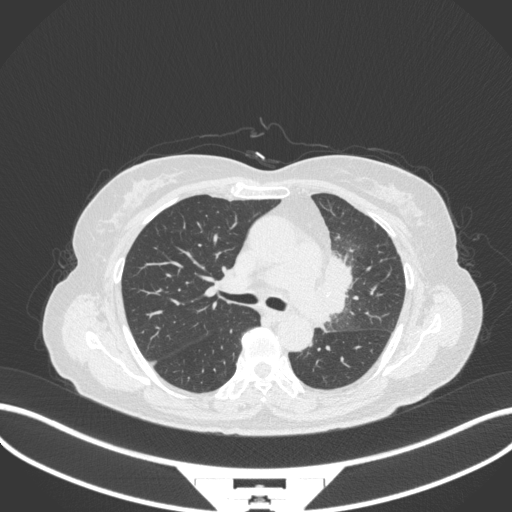
Chest CT, one axial slice; slice 210 of 382 in the series (ordered by position); reconstruction kernel B31f; lung window (W 1500 / L -600 HU); 1 mm slice thickness; 512 × 512 image matrix, field of view 400 × 400 mm. Patient: female, 64 years. From the clinical record (not read from this slice): clinical TNM (as recorded): T2a N2 M0.
Outlined on this slice (rectangle marked by the reading radiologist):
- lung tumour (recorded histology: adenocarcinoma): bounding box [x1, y1, x2, y2] px = [314, 237, 355, 329]